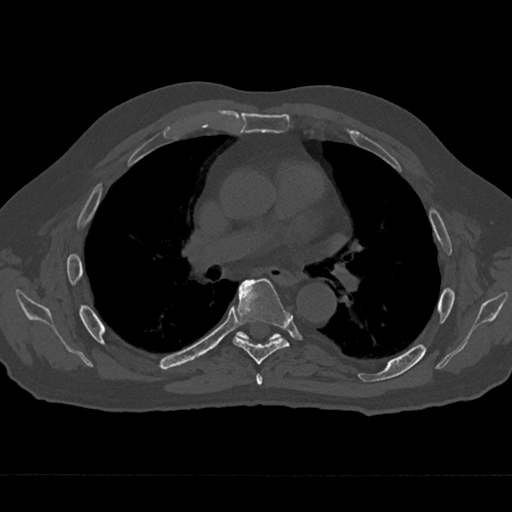
CT including the spine, one axial slice; position 411 of 797 along the scan axis; 120 kVp; bone window (W 1800 / L 400 HU); 0.5 mm slice thickness; 512 × 512 image matrix, field of view 377 × 377 mm. Patient: male, 75 years. From the clinical record (not read from this slice): primary cancer: renal.
Outlined on this slice (semi-automatic segmentation, software-assisted and operator-edited):
- T5 vertebra: box from (x=256, y=373) to (x=263, y=385) px
- T6 vertebra: (x=233, y=278)–(x=291, y=365)
- T7 vertebra: (x=238, y=331)–(x=279, y=341)